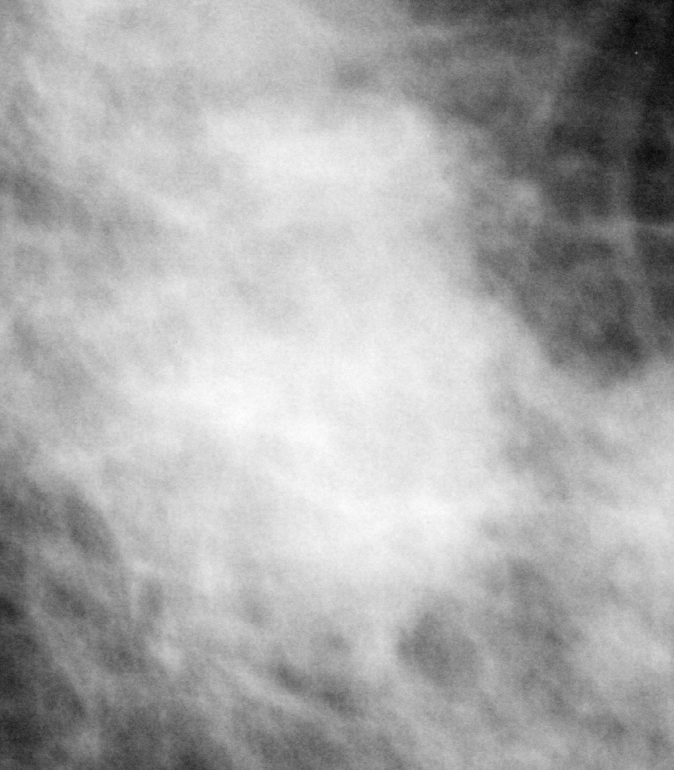
Cropped region of a digitized screen-film mammogram centred on a radiologist-marked abnormality, left breast, MLO view, BI-RADS breast density category 2 (scale 1–4).
Finding: mass, shape irregular, margins ill defined; BI-RADS assessment category 5; subtlety rating 5 on a 1 (subtle) to 5 (obvious) scale; pathology result (as recorded, not read from the image): malignant.